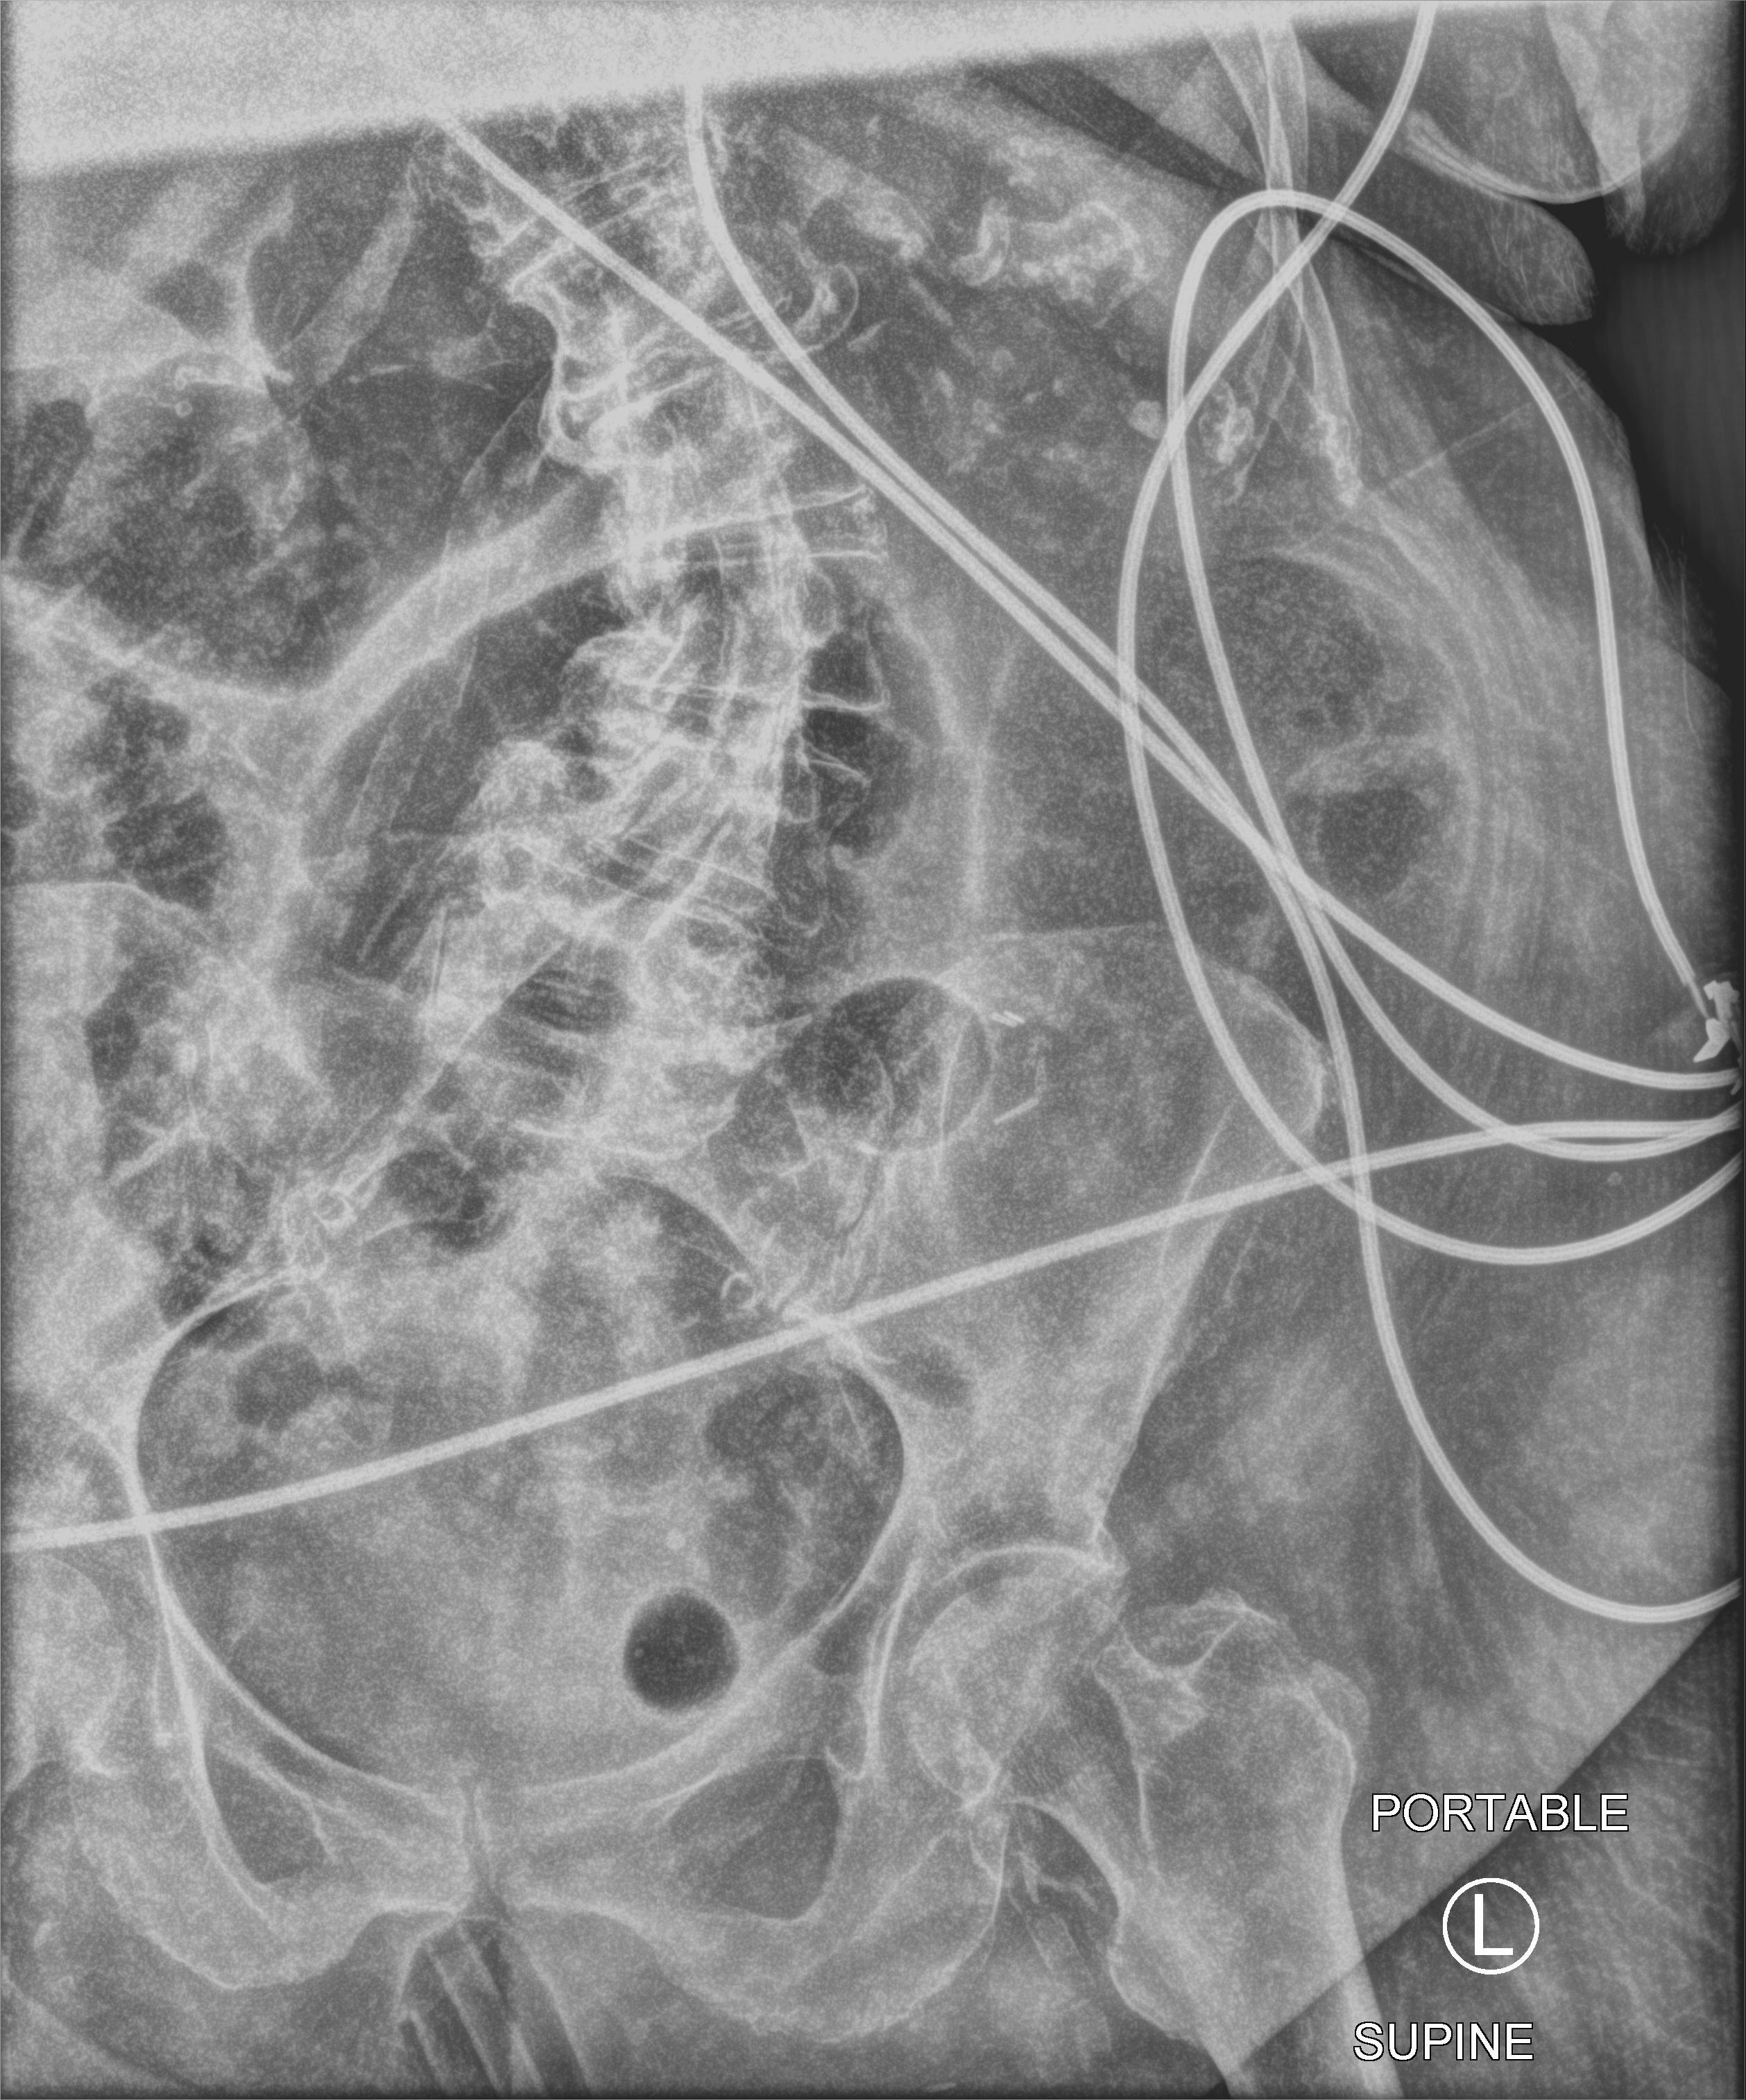
Portable abdomen radiograph, anteroposterior (AP) projection. Female patient hospitalised with COVID-19, age 75–90 years.
From the hospital-stay record, not from the radiograph (when in the stay this image was taken is not recorded): length of hospital stay: 10 days; admitted to intensive care during this hospital stay: no.